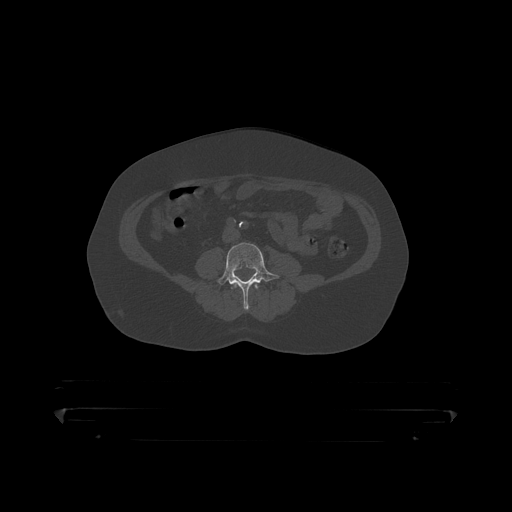
CT including the spine, one axial slice; position 66 of 390 along the scan axis; bone window (W 1800 / L 400 HU); 512 × 512 image matrix. Patient: male, 60 years. From the clinical record (not read from this slice): primary cancer: prostate.
Annotated regions visible in this slice (semi-automatic segmentation, software-assisted and operator-edited):
- L3 vertebra: bounding box (x1, y1, x2, y2) in pixels: (231, 283, 262, 298)
- L4 vertebra: (216, 243, 281, 311)